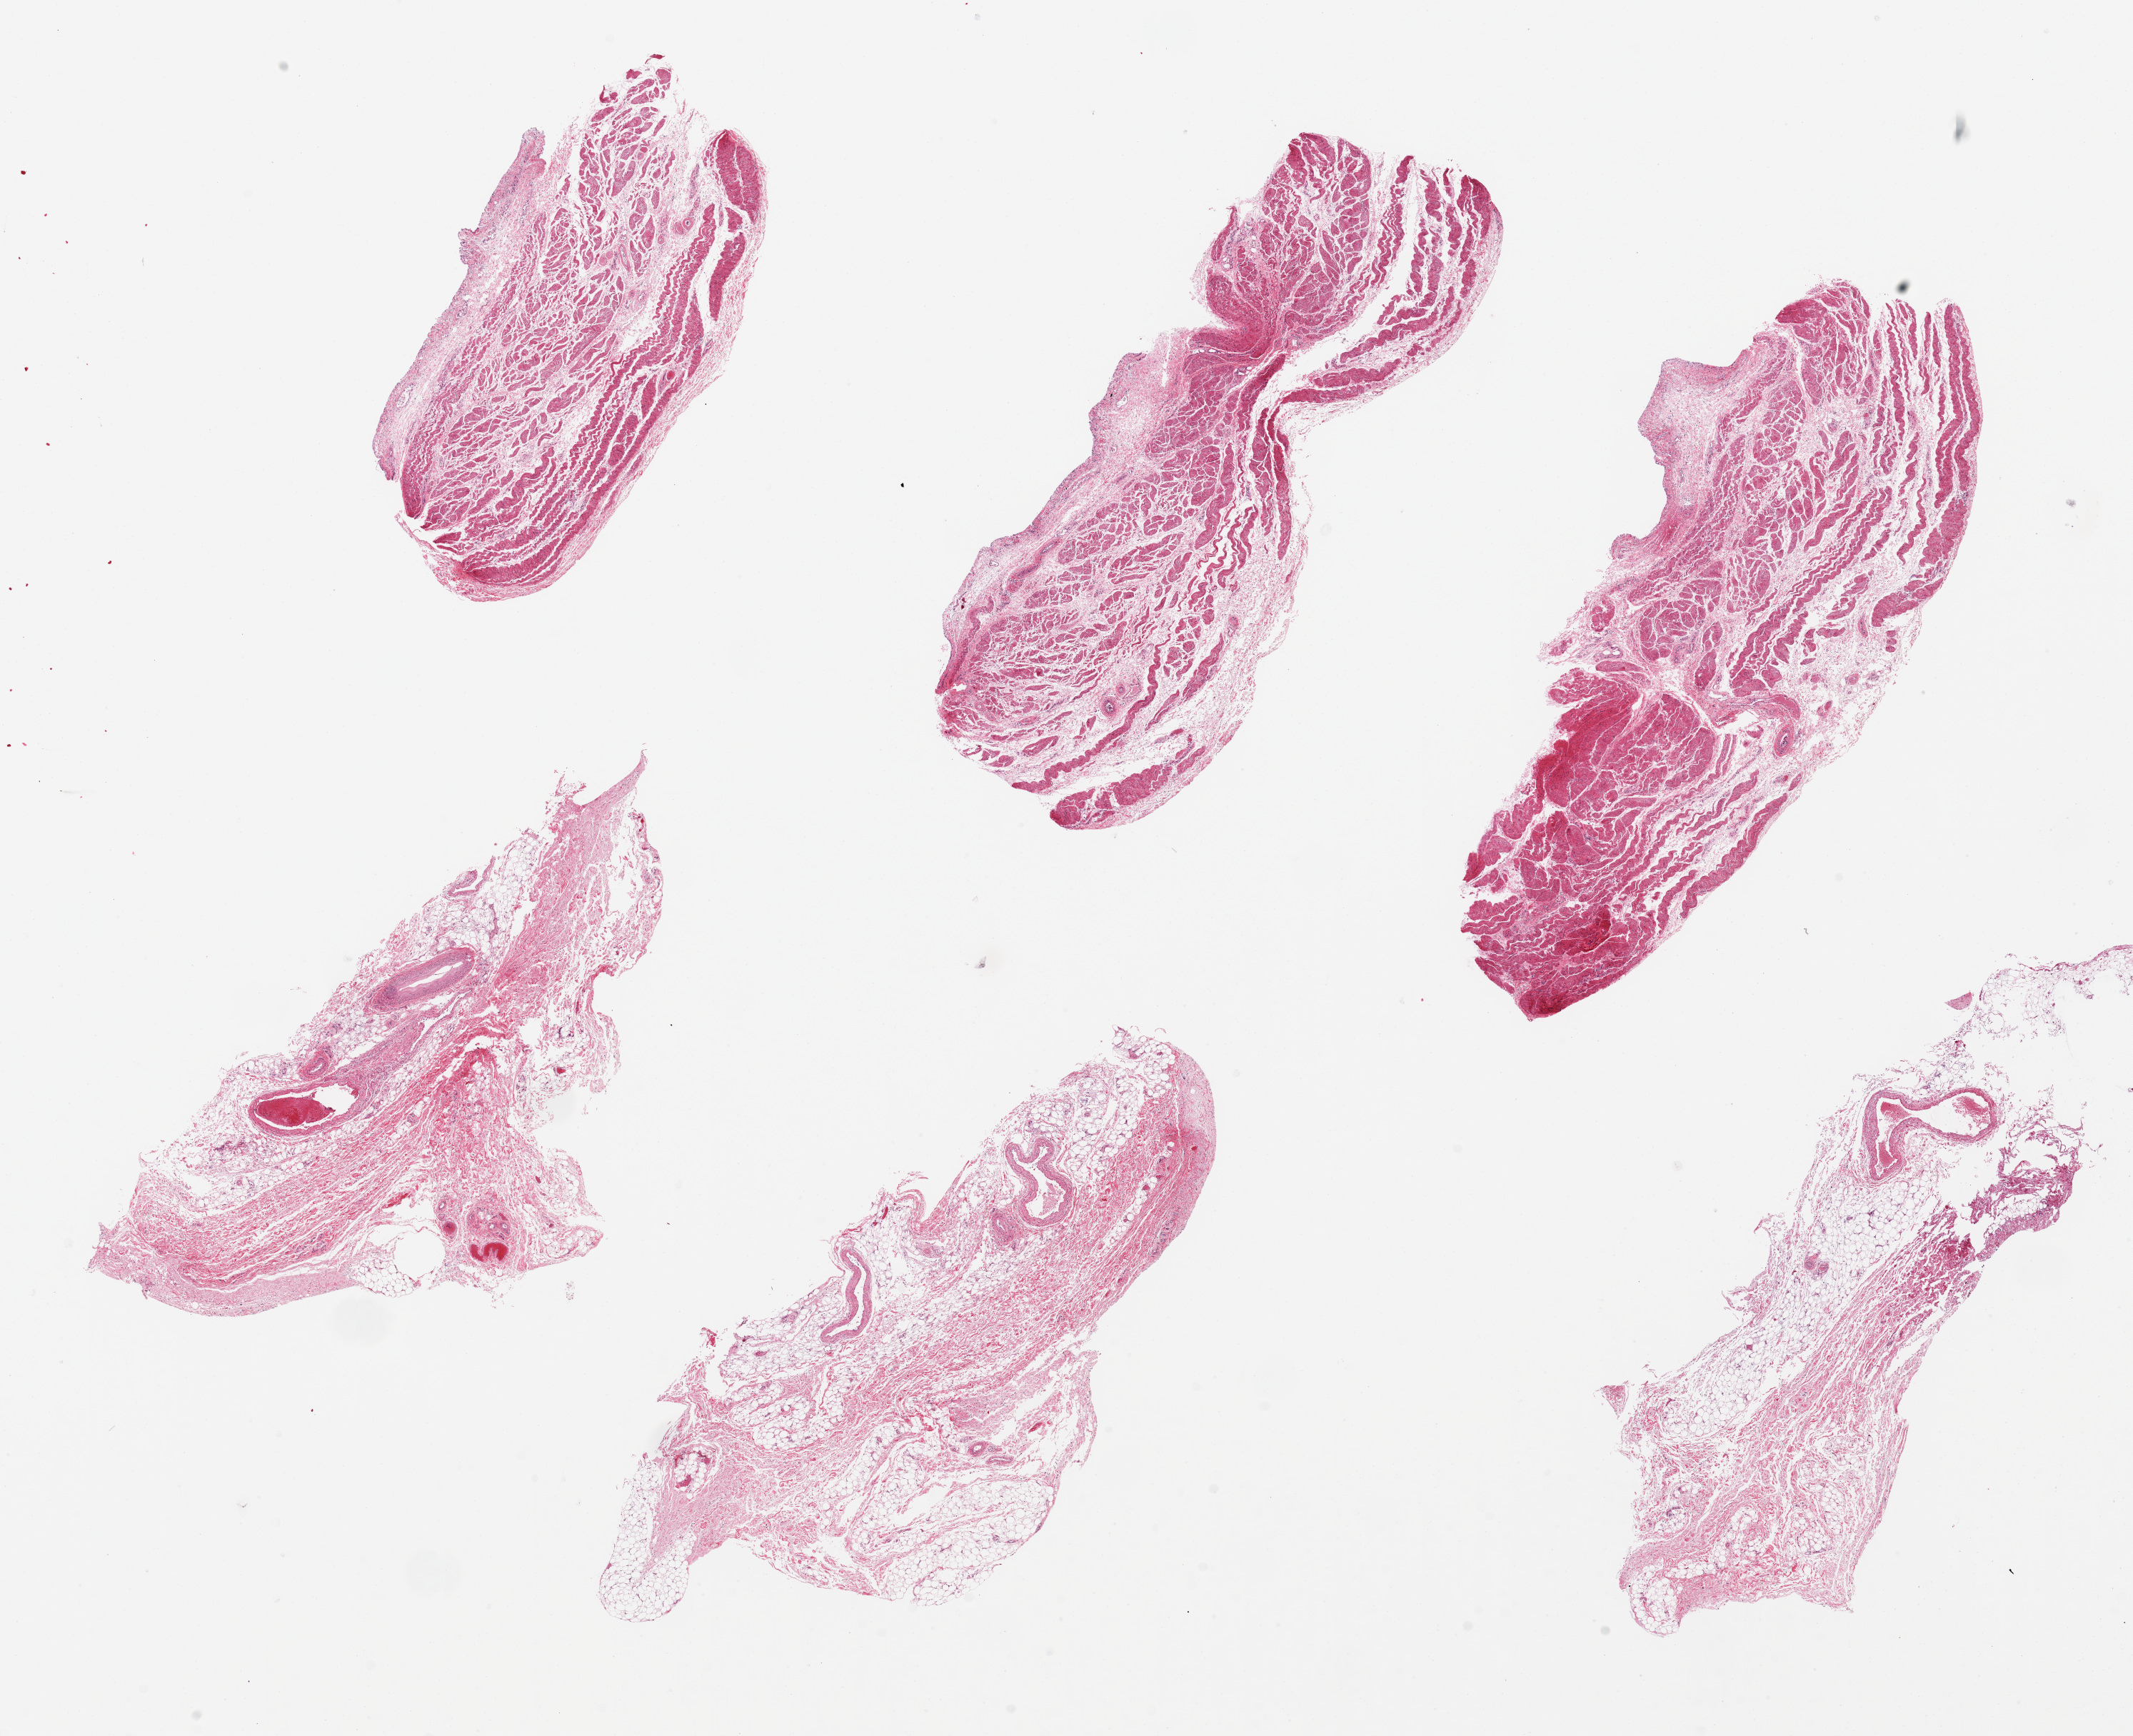
Haematoxylin and eosin whole-slide image, brightfield — low-resolution overview of the scanned area, about 23.6 x 19.2 mm (slide scanned at 20x). PAXgene-fixed paraffin-embedded (PFPE) section. Section of urinary bladder (target tissue). Donor tissue sample. Donor: male.
Review note (as recorded): 6 pieces up to 9x4 mm; all epithelium sloughed.